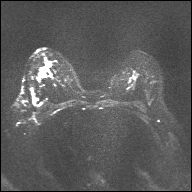
Breast MRI, one axial slice; position 19 of 32 along the scan axis; diffusion-weighted series; image 2 of 4 stored at this slice position (different b-values; order by instance number); 1.5 T; 192 × 192 image matrix, field of view 360 × 360 mm. Female patient.
Outlined on this slice (outlined manually by an expert reader):
- tumour on diffusion-weighted imaging: box from (x=42, y=72) to (x=46, y=77) px